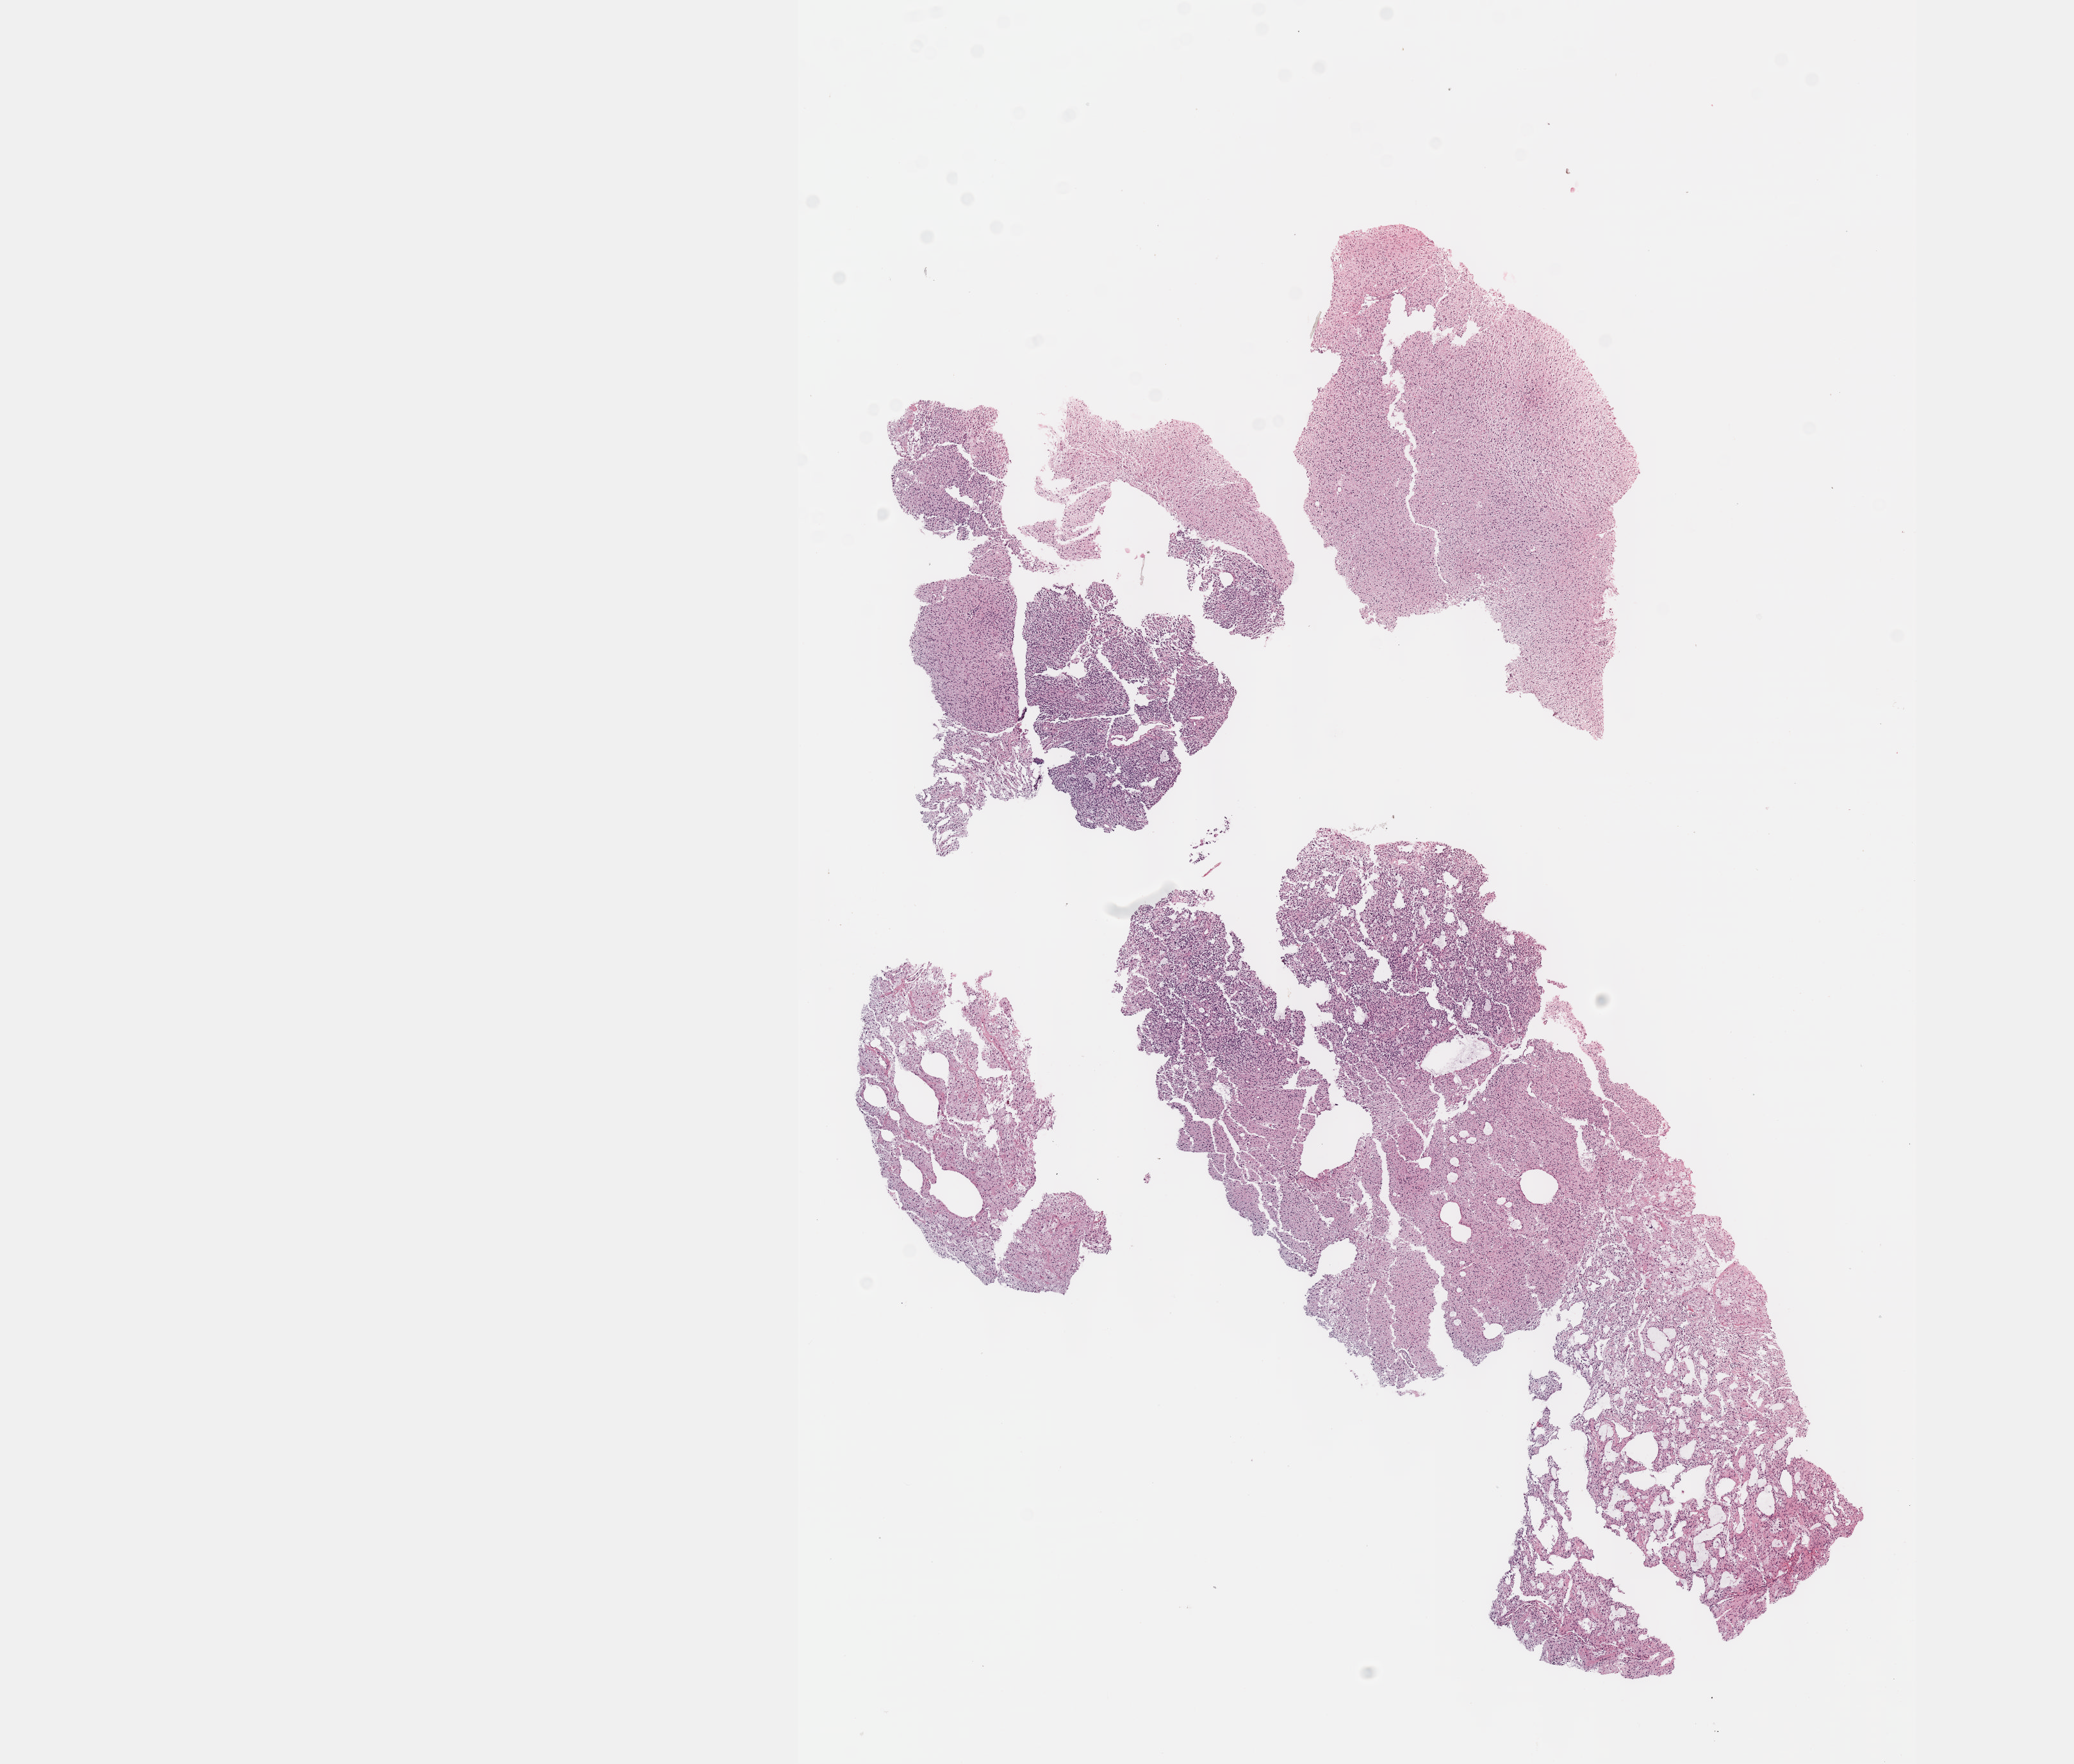
H&E-stained whole-slide image, a low-resolution overview of the entire scanned area, about 13.1 x 11.1 mm (slide scanned at 40x), formalin-fixed paraffin-embedded (FFPE) diagnostic section, sample: primary tumour, brain. Patient: female, age at initial diagnosis 41 years. Histologic grade: G2 (moderately differentiated).
- diagnosis: Oligodendroglioma, NOS (cerebrum)